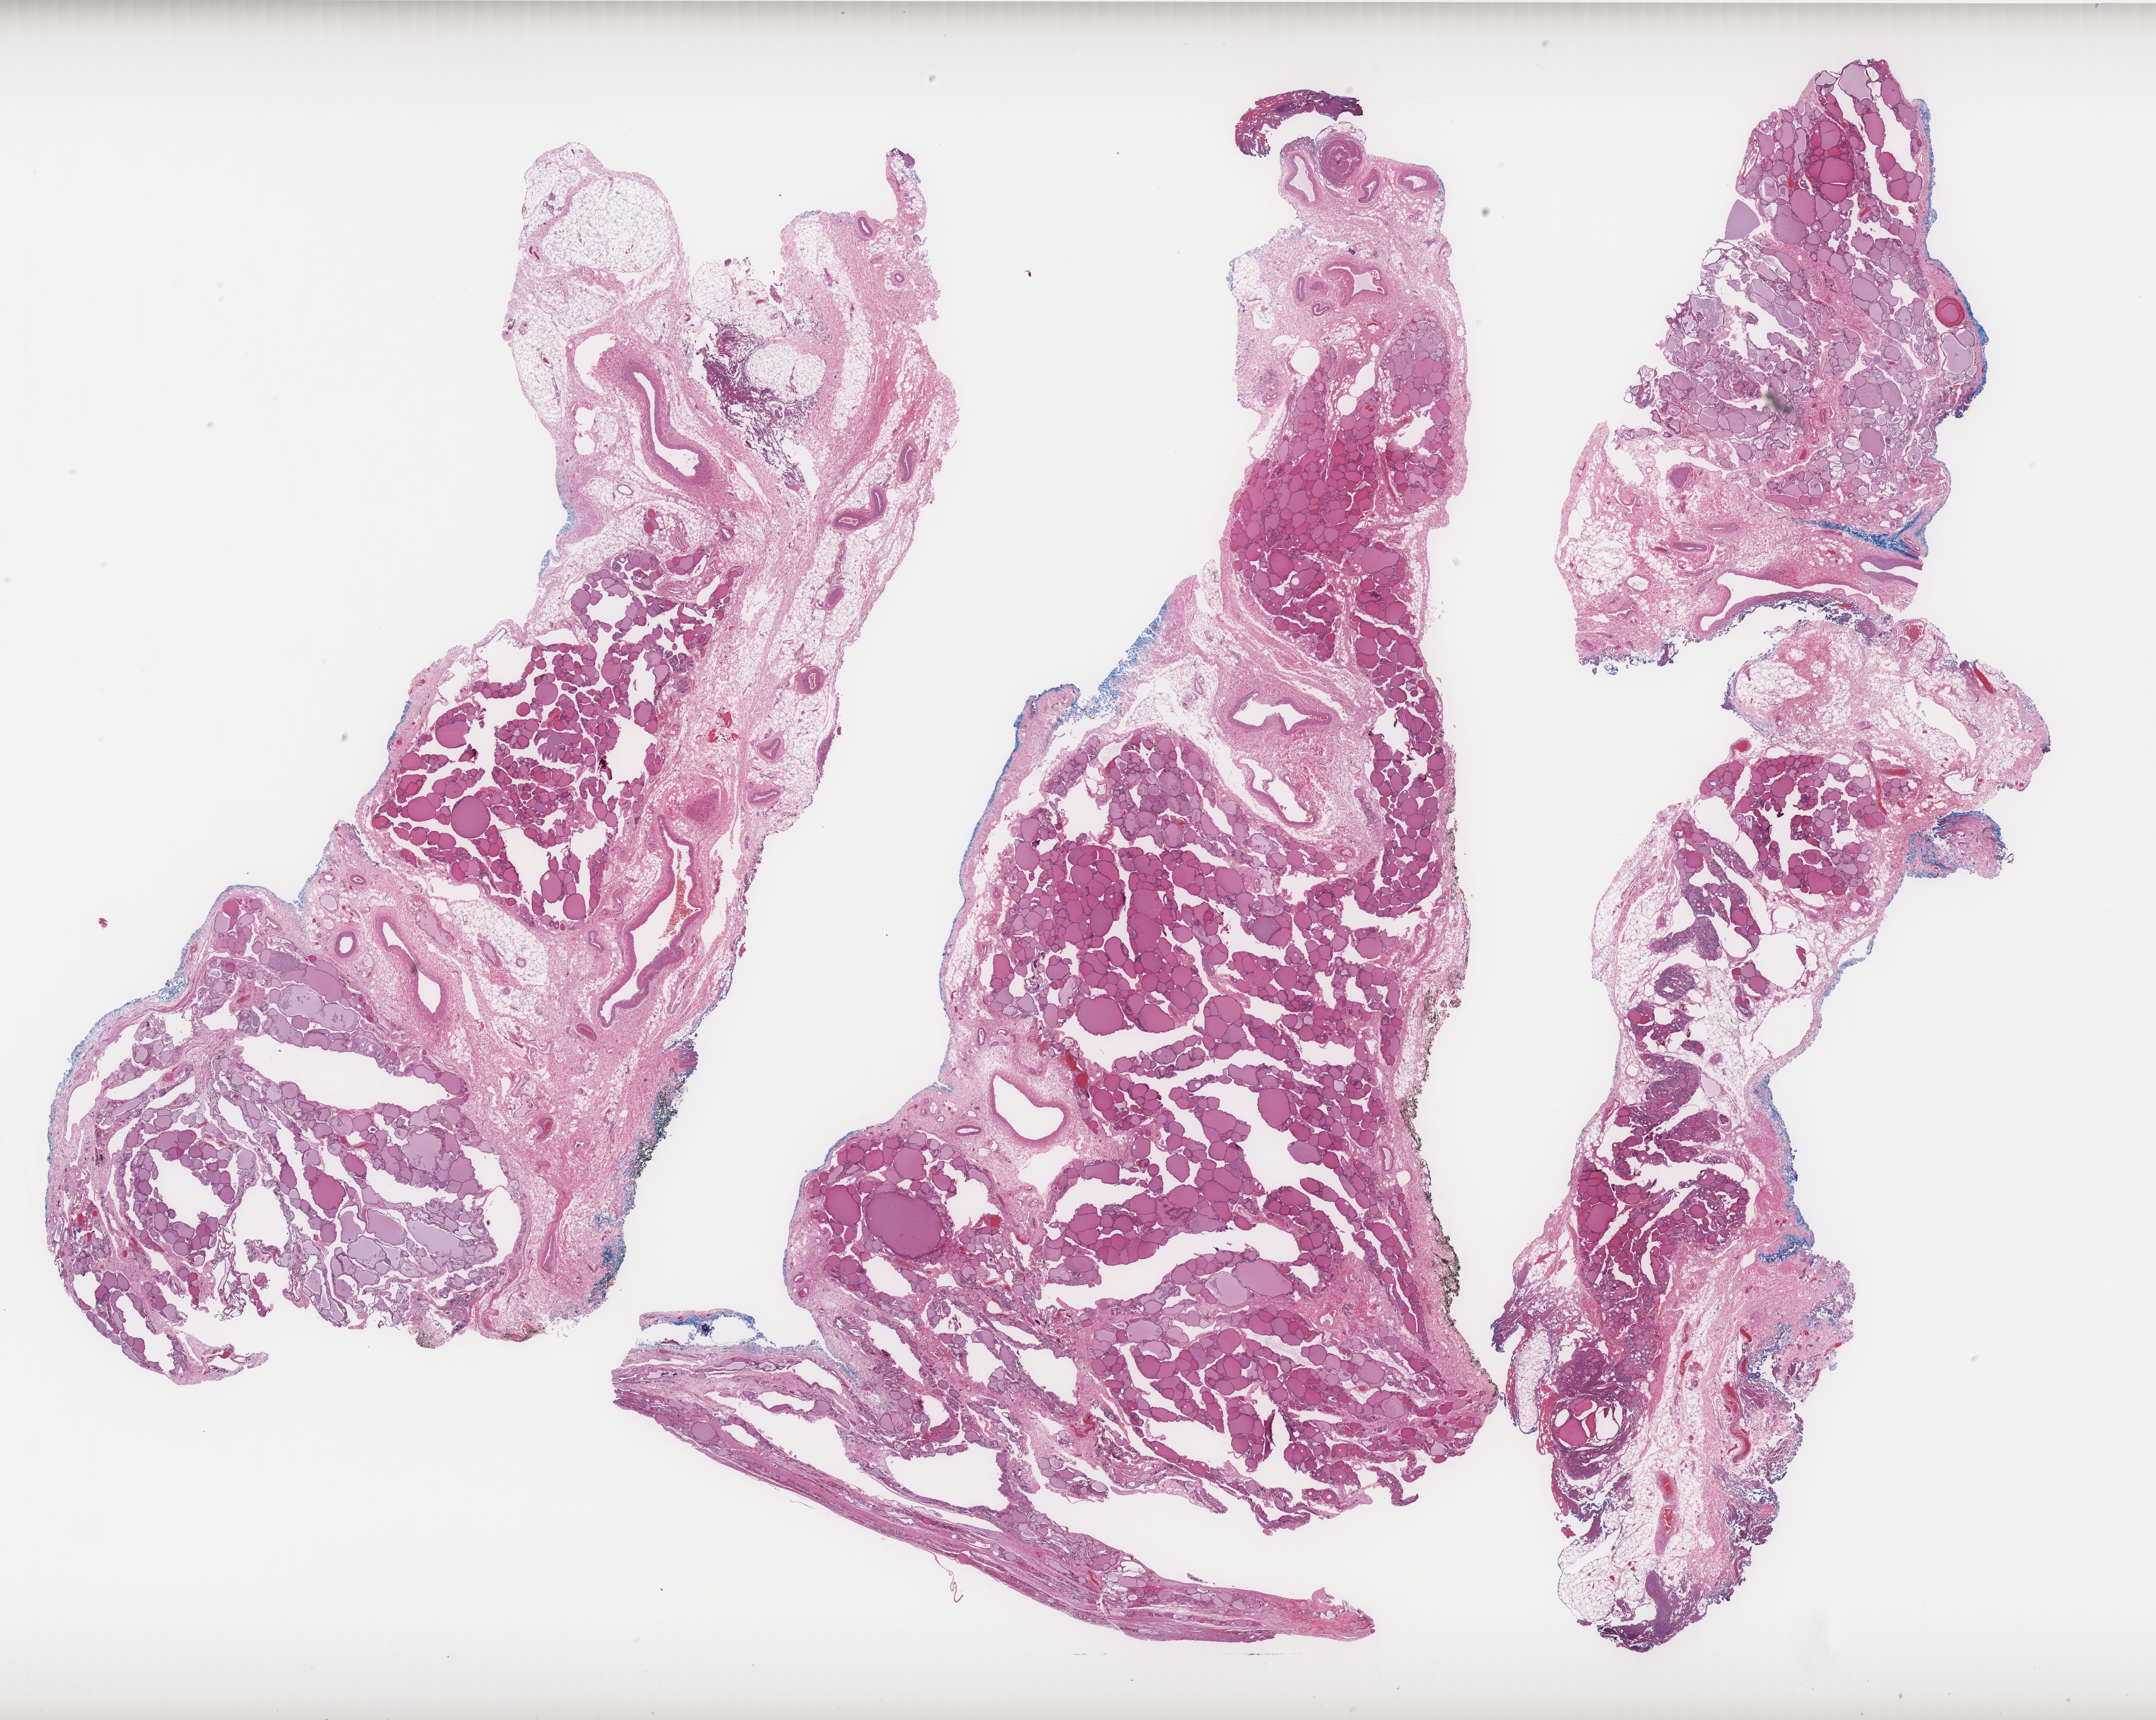
Hematoxylin and eosin (H&E) stained whole-slide image — a low-resolution overview of the entire scanned area, about 27.4 x 21.9 mm, FFPE section, thyroid, primary tumour sample. Female, age 54 years at initial diagnosis.
Histologic diagnosis: Oxyphilic adenocarcinoma. AJCC pathologic stage: III (7th edition). Laterality: left.